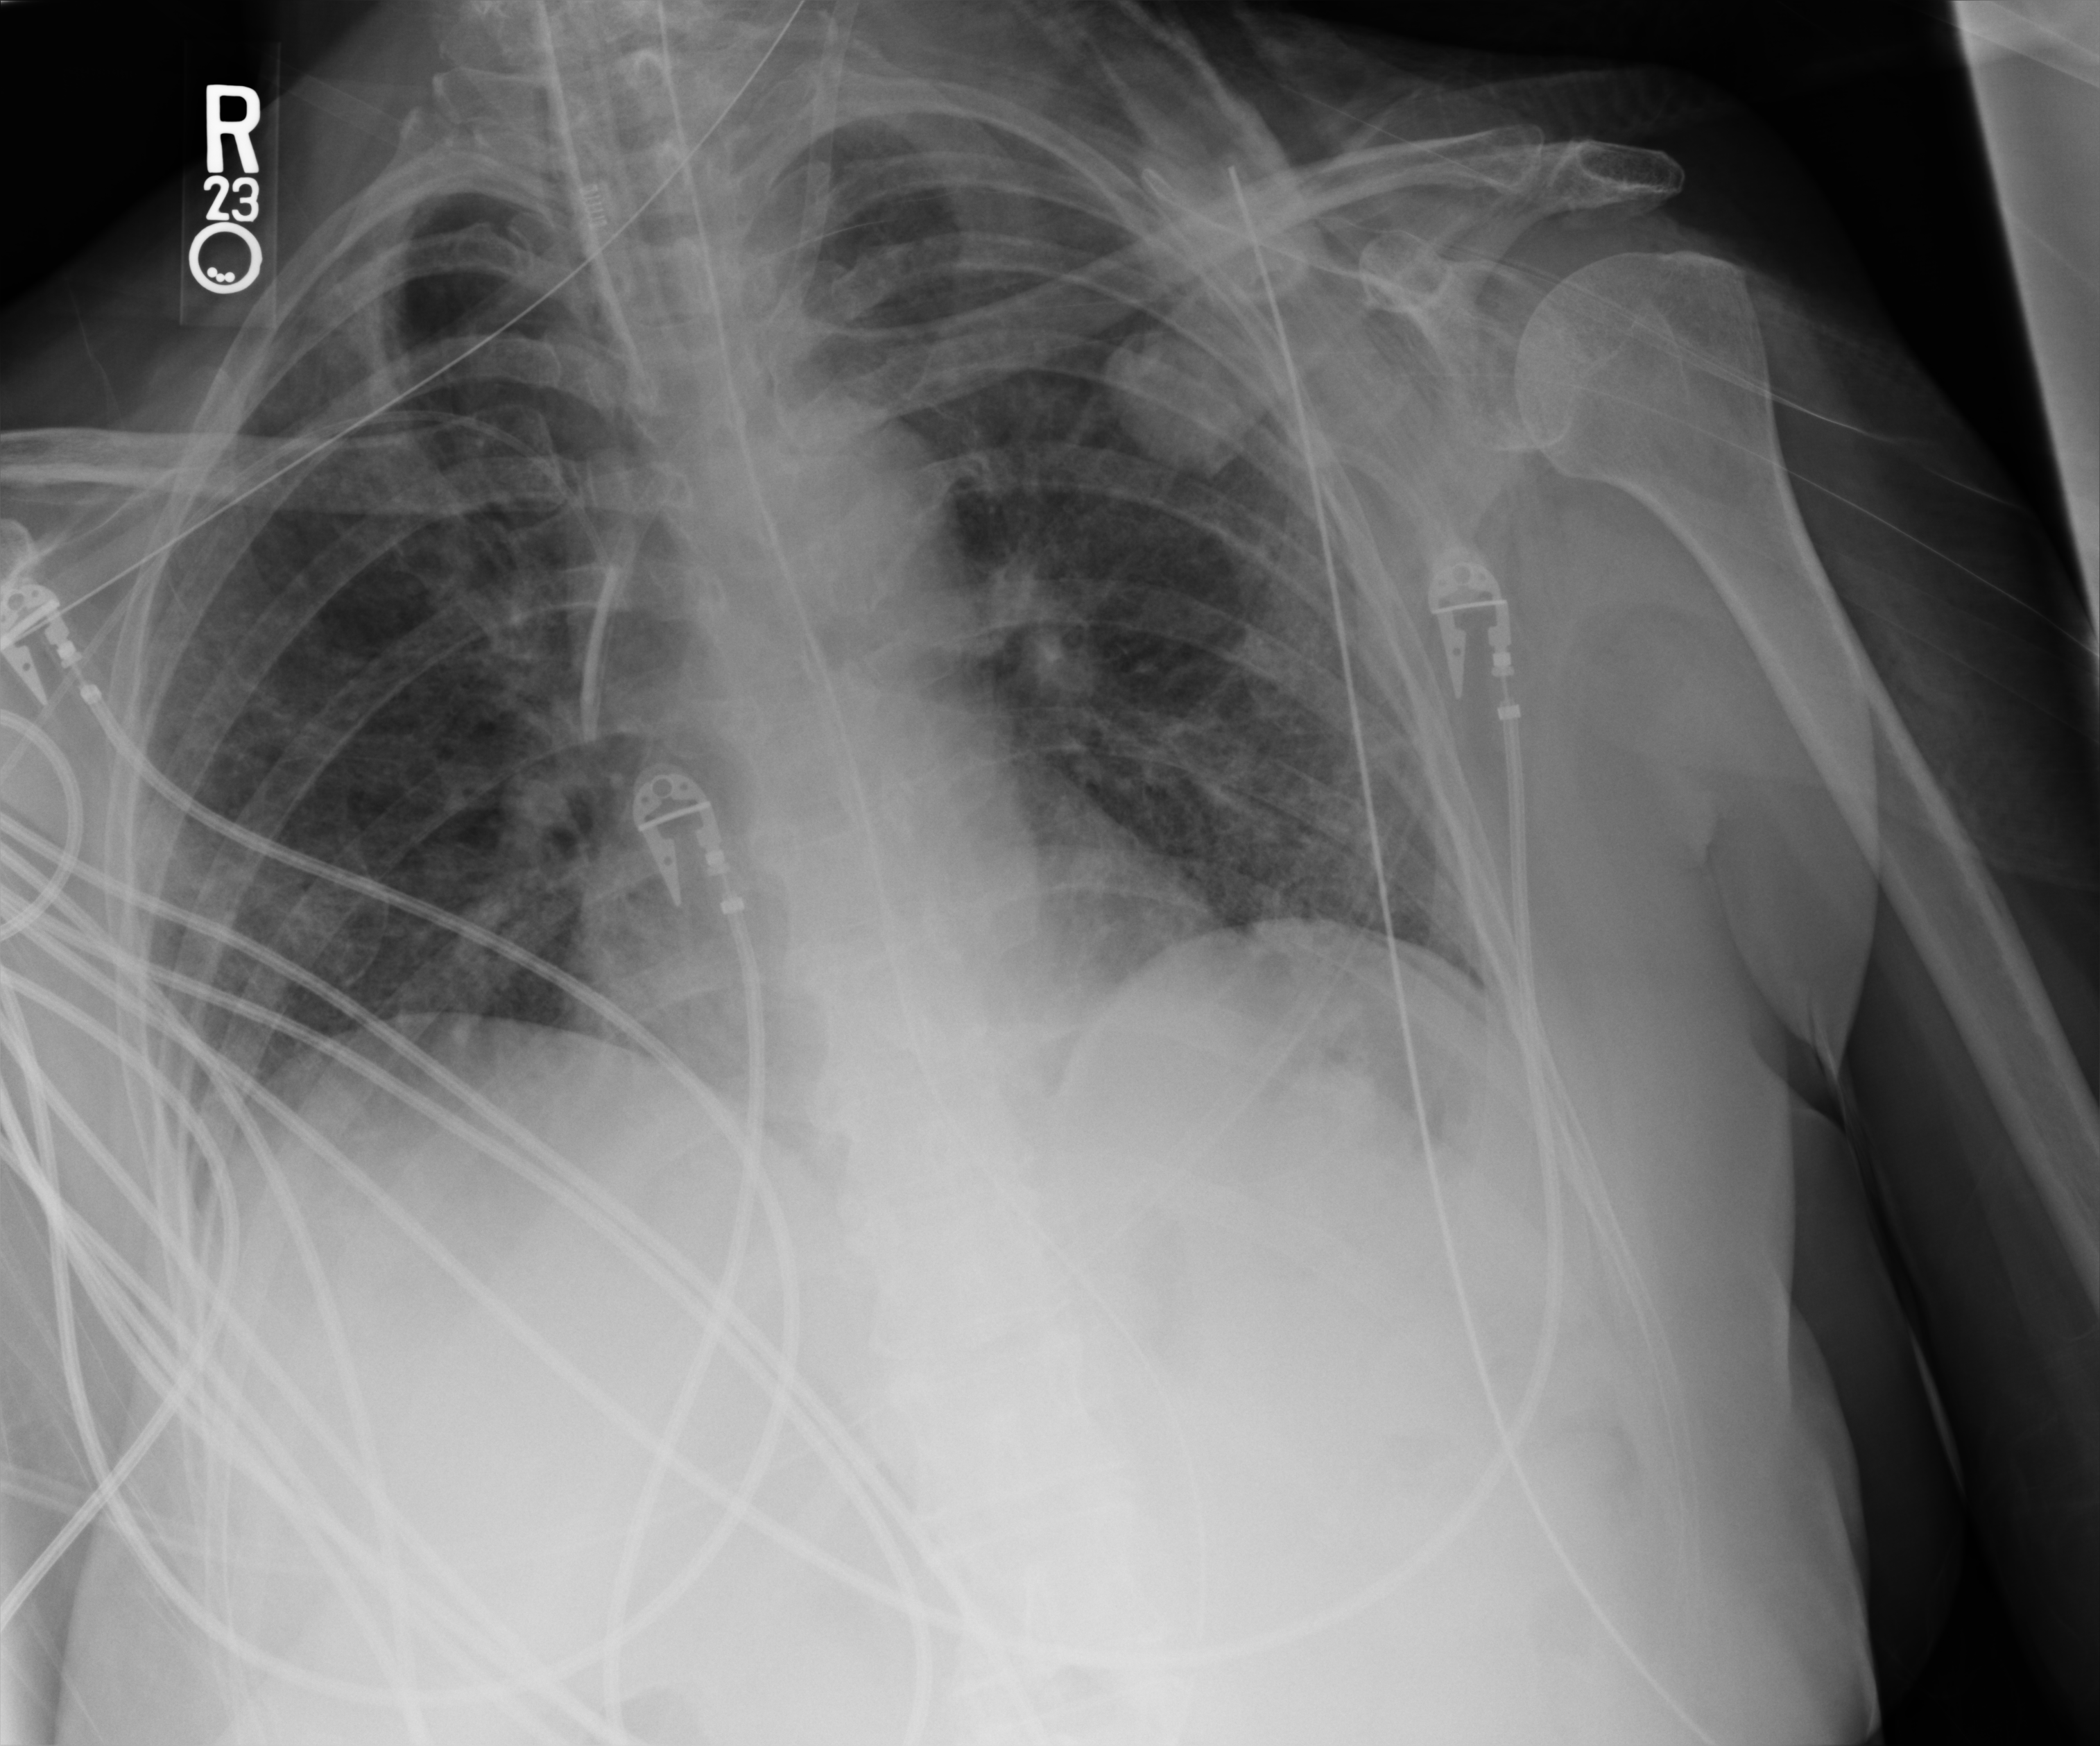
Portable chest radiograph, anteroposterior (AP) projection. Female patient hospitalised with COVID-19, age 60–74 years.
Hospital-stay facts (about this admission, not read from this image; timing relative to this image not recorded): length of hospital stay: 43 days; admitted to intensive care during this hospital stay: yes; hypertension (admission record): yes.